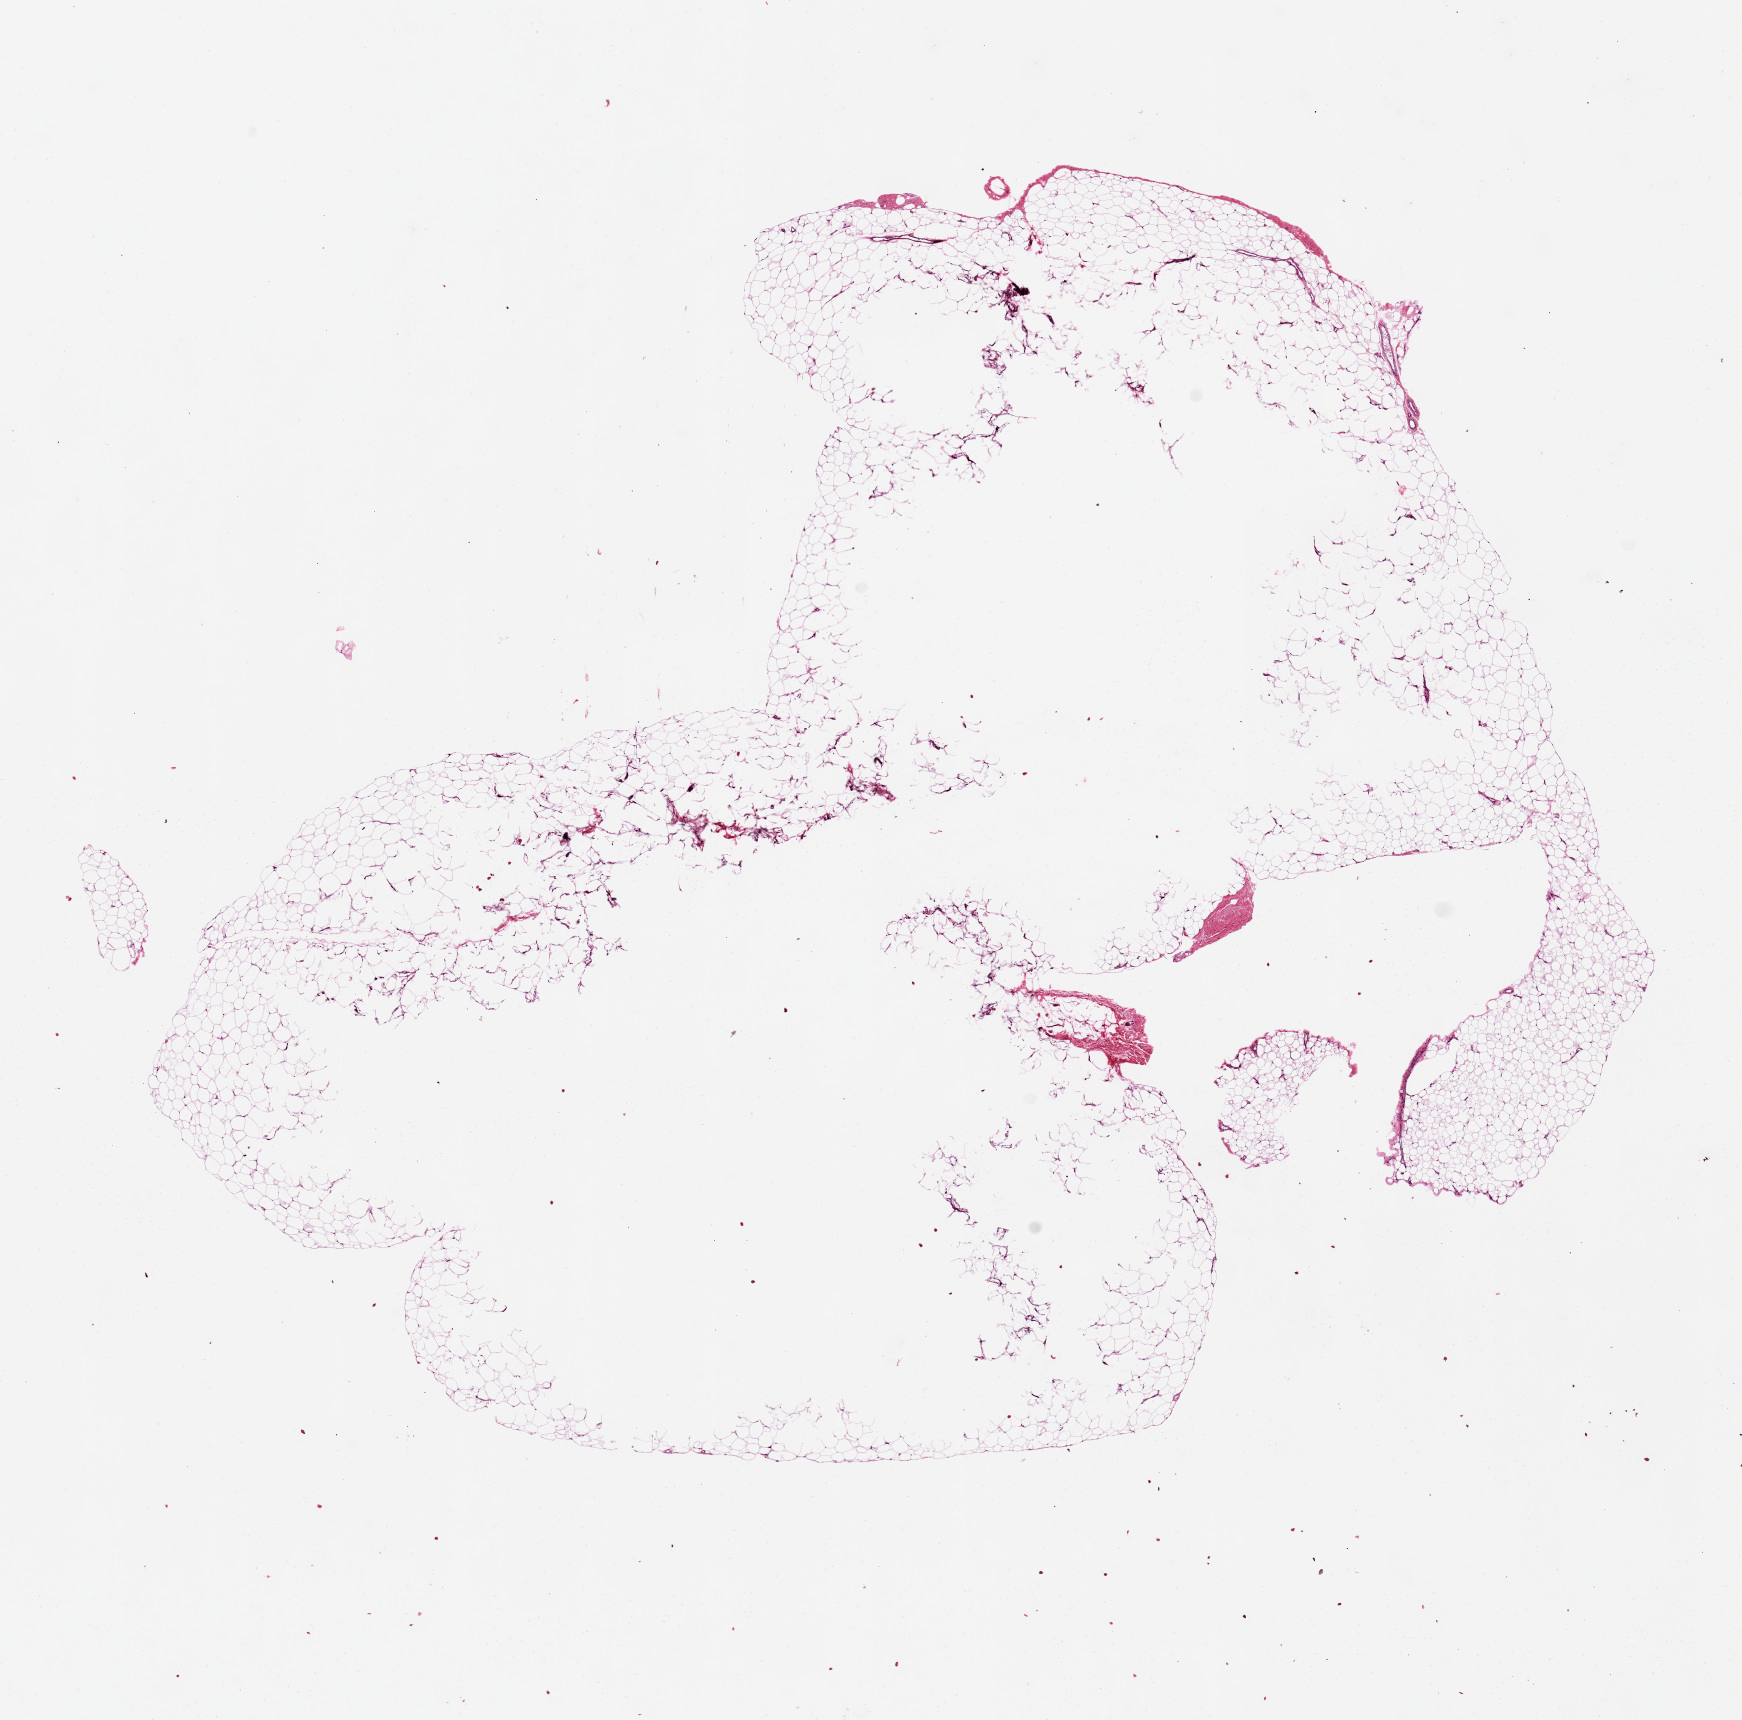
Haematoxylin and eosin whole-slide image, brightfield, whole scanned area (about 13.8 x 13.6 mm, slide scanned at 20x) shown as a low-resolution overview; PAXgene-fixed paraffin-embedded (PFPE) section; section of adipose tissue (target tissue); donor tissue sample. Donor: male.
Review note (as recorded): Specimen appears underfixed; central holes/tears.